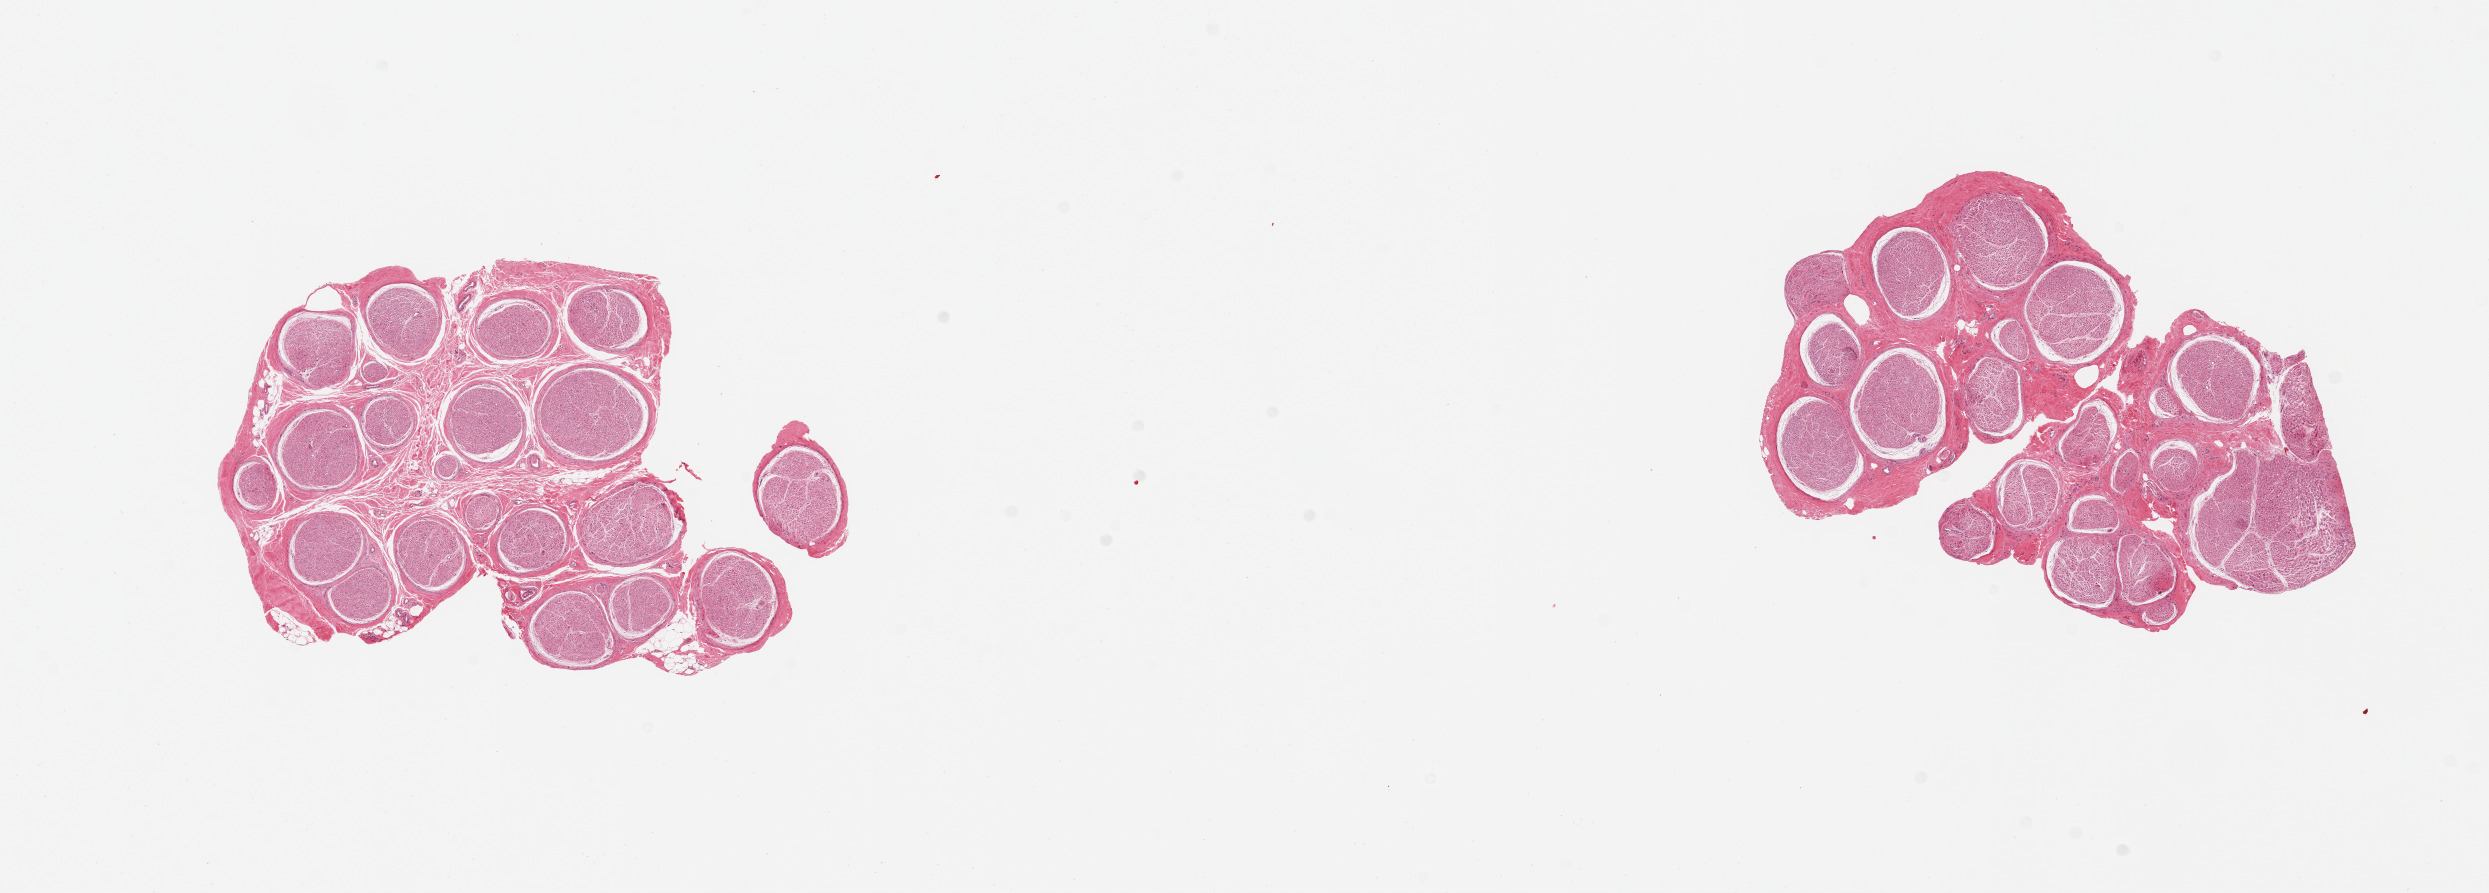
Hematoxylin and eosin (H&E) whole-slide image — a low-resolution overview of the entire scanned area, about 19.7 x 7.1 mm, PAXgene-fixed, paraffin-embedded tissue, section of tibial nerve (target tissue), donor tissue sample. Donor sex: male.
Reviewer comment on this tissue sample: 2 pieces; well trimmed.